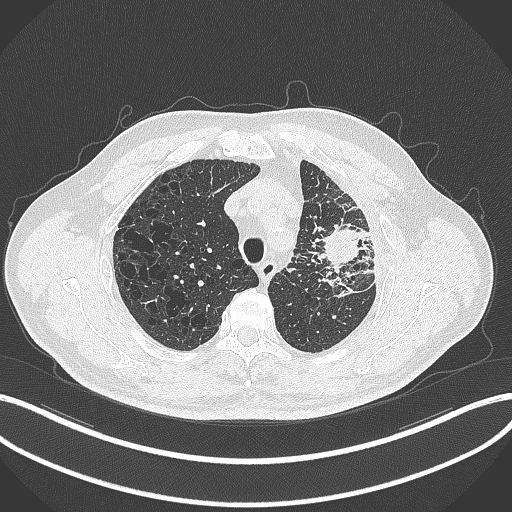
Chest CT, one axial slice. Position 254 of 297 along the scan axis. Reconstruction kernel B70f. Lung window (W 1500 / L -600 HU). 512 × 512 image matrix, field of view 400 × 400 mm. Male patient, age 68 years. Case-level facts recorded for this patient, not image findings: clinical TNM (as recorded): T3 N3 M1.
Structures marked on this image (rectangle marked by the reading radiologist):
- lung tumour (recorded histology: adenocarcinoma): box from (x=319, y=216) to (x=364, y=274) px